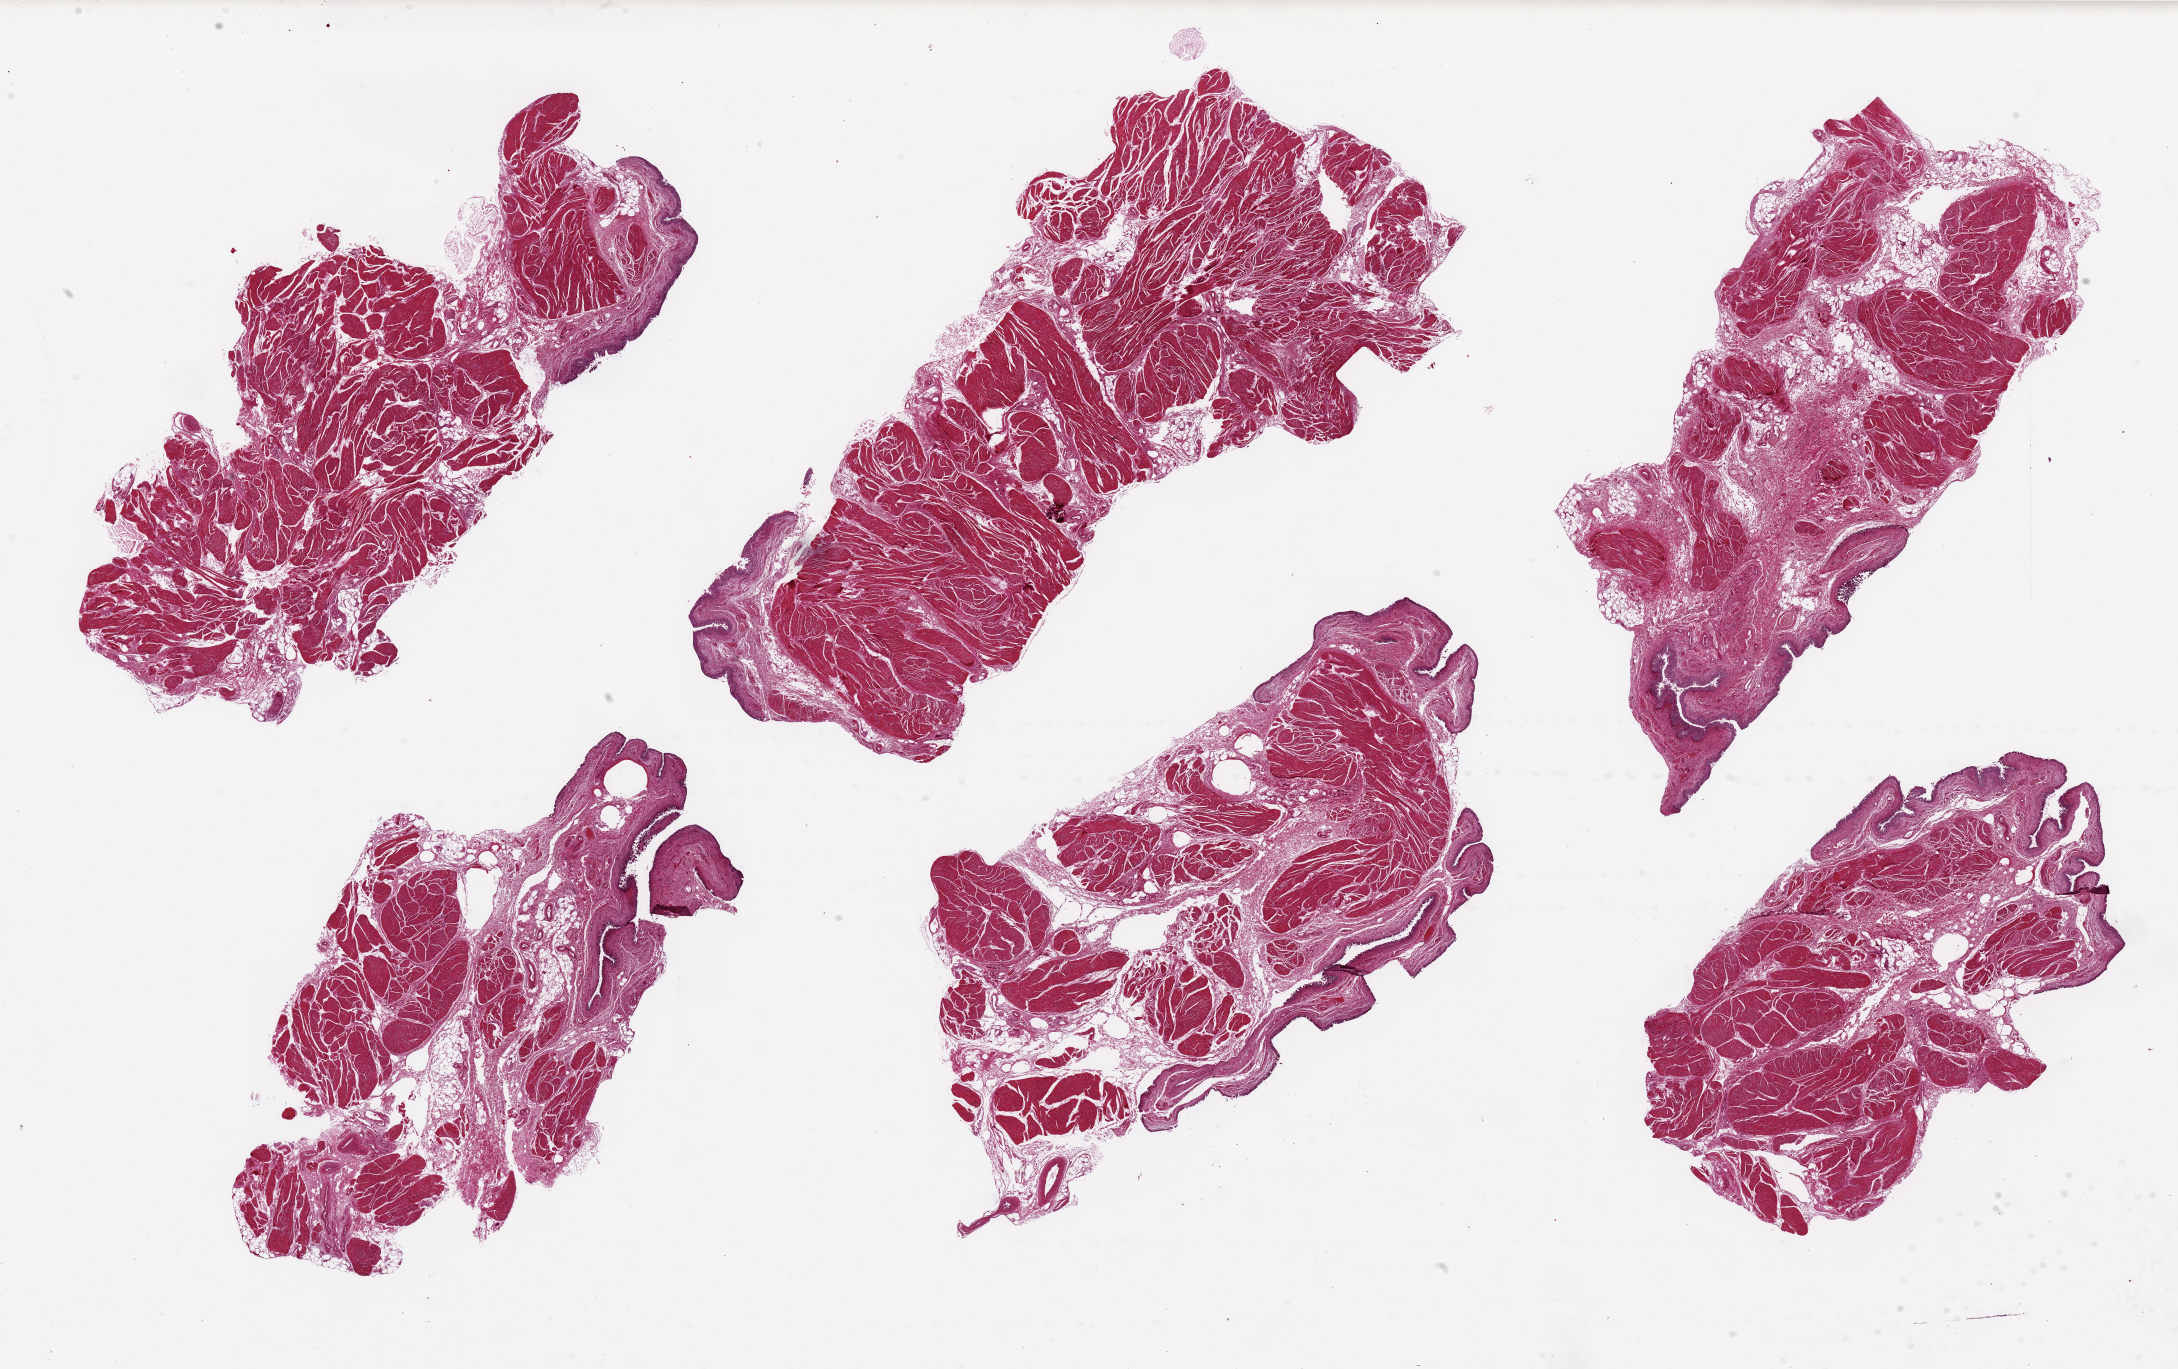
Haematoxylin and eosin whole-slide image, low-resolution overview of the scanned area, about 34.5 x 21.7 mm; PAXgene-fixed paraffin-embedded (PFPE) section; target tissue: urinary bladder; tissue donor sample. Male donor.
- pathologist's review note for this sample: 6 pieces up to 12x6 mm; cassette marking on tissue due to 'snug fit' in cassette; considerable epithelial sloughing